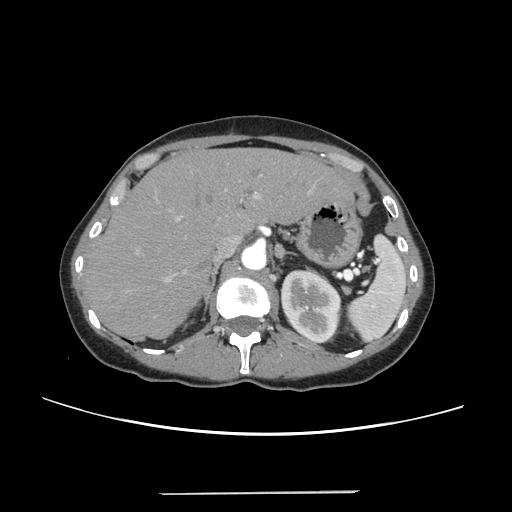
Contrast-enhanced abdominal CT, one axial slice; position 170 of 240 along the scan axis; intravenous contrast given; soft-tissue window (W 400 / L 40 HU); 512 × 512 image matrix, field of view 371 × 371 mm. Female patient, age 60 years. Case-level facts recorded for this patient, not image findings: diagnosis: colorectal cancer liver metastases, imaged before liver resection; multiple liver metastases: no; largest metastasis: 1.5 cm; disease in both lobes: no.
Outlined on this slice (outlined manually by an expert reader):
- liver: bounding box [x1, y1, x2, y2] px = [86, 149, 349, 338]
- planned liver remnant (the part of the liver to remain after resection): [86, 149, 348, 338]
- portal vein (with intrahepatic branches): [137, 172, 312, 283]